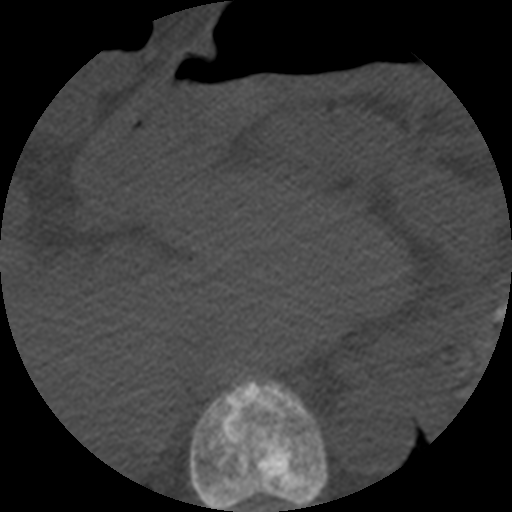
CT including the spine, one axial slice; slice 260 of 508 in the series (ordered by position); 120 kVp; bone window (W 1800 / L 400 HU); 1.25 mm slice thickness; 512 × 512 image matrix, field of view 160 × 160 mm. Patient age 57 years. From the clinical record (not read from this slice): primary cancer: prostate.
Outlined on this slice (semi-automatic segmentation, software-assisted and operator-edited):
- T10 vertebra: bounding box <189,377,328,512> (left, top, right, bottom; pixels)